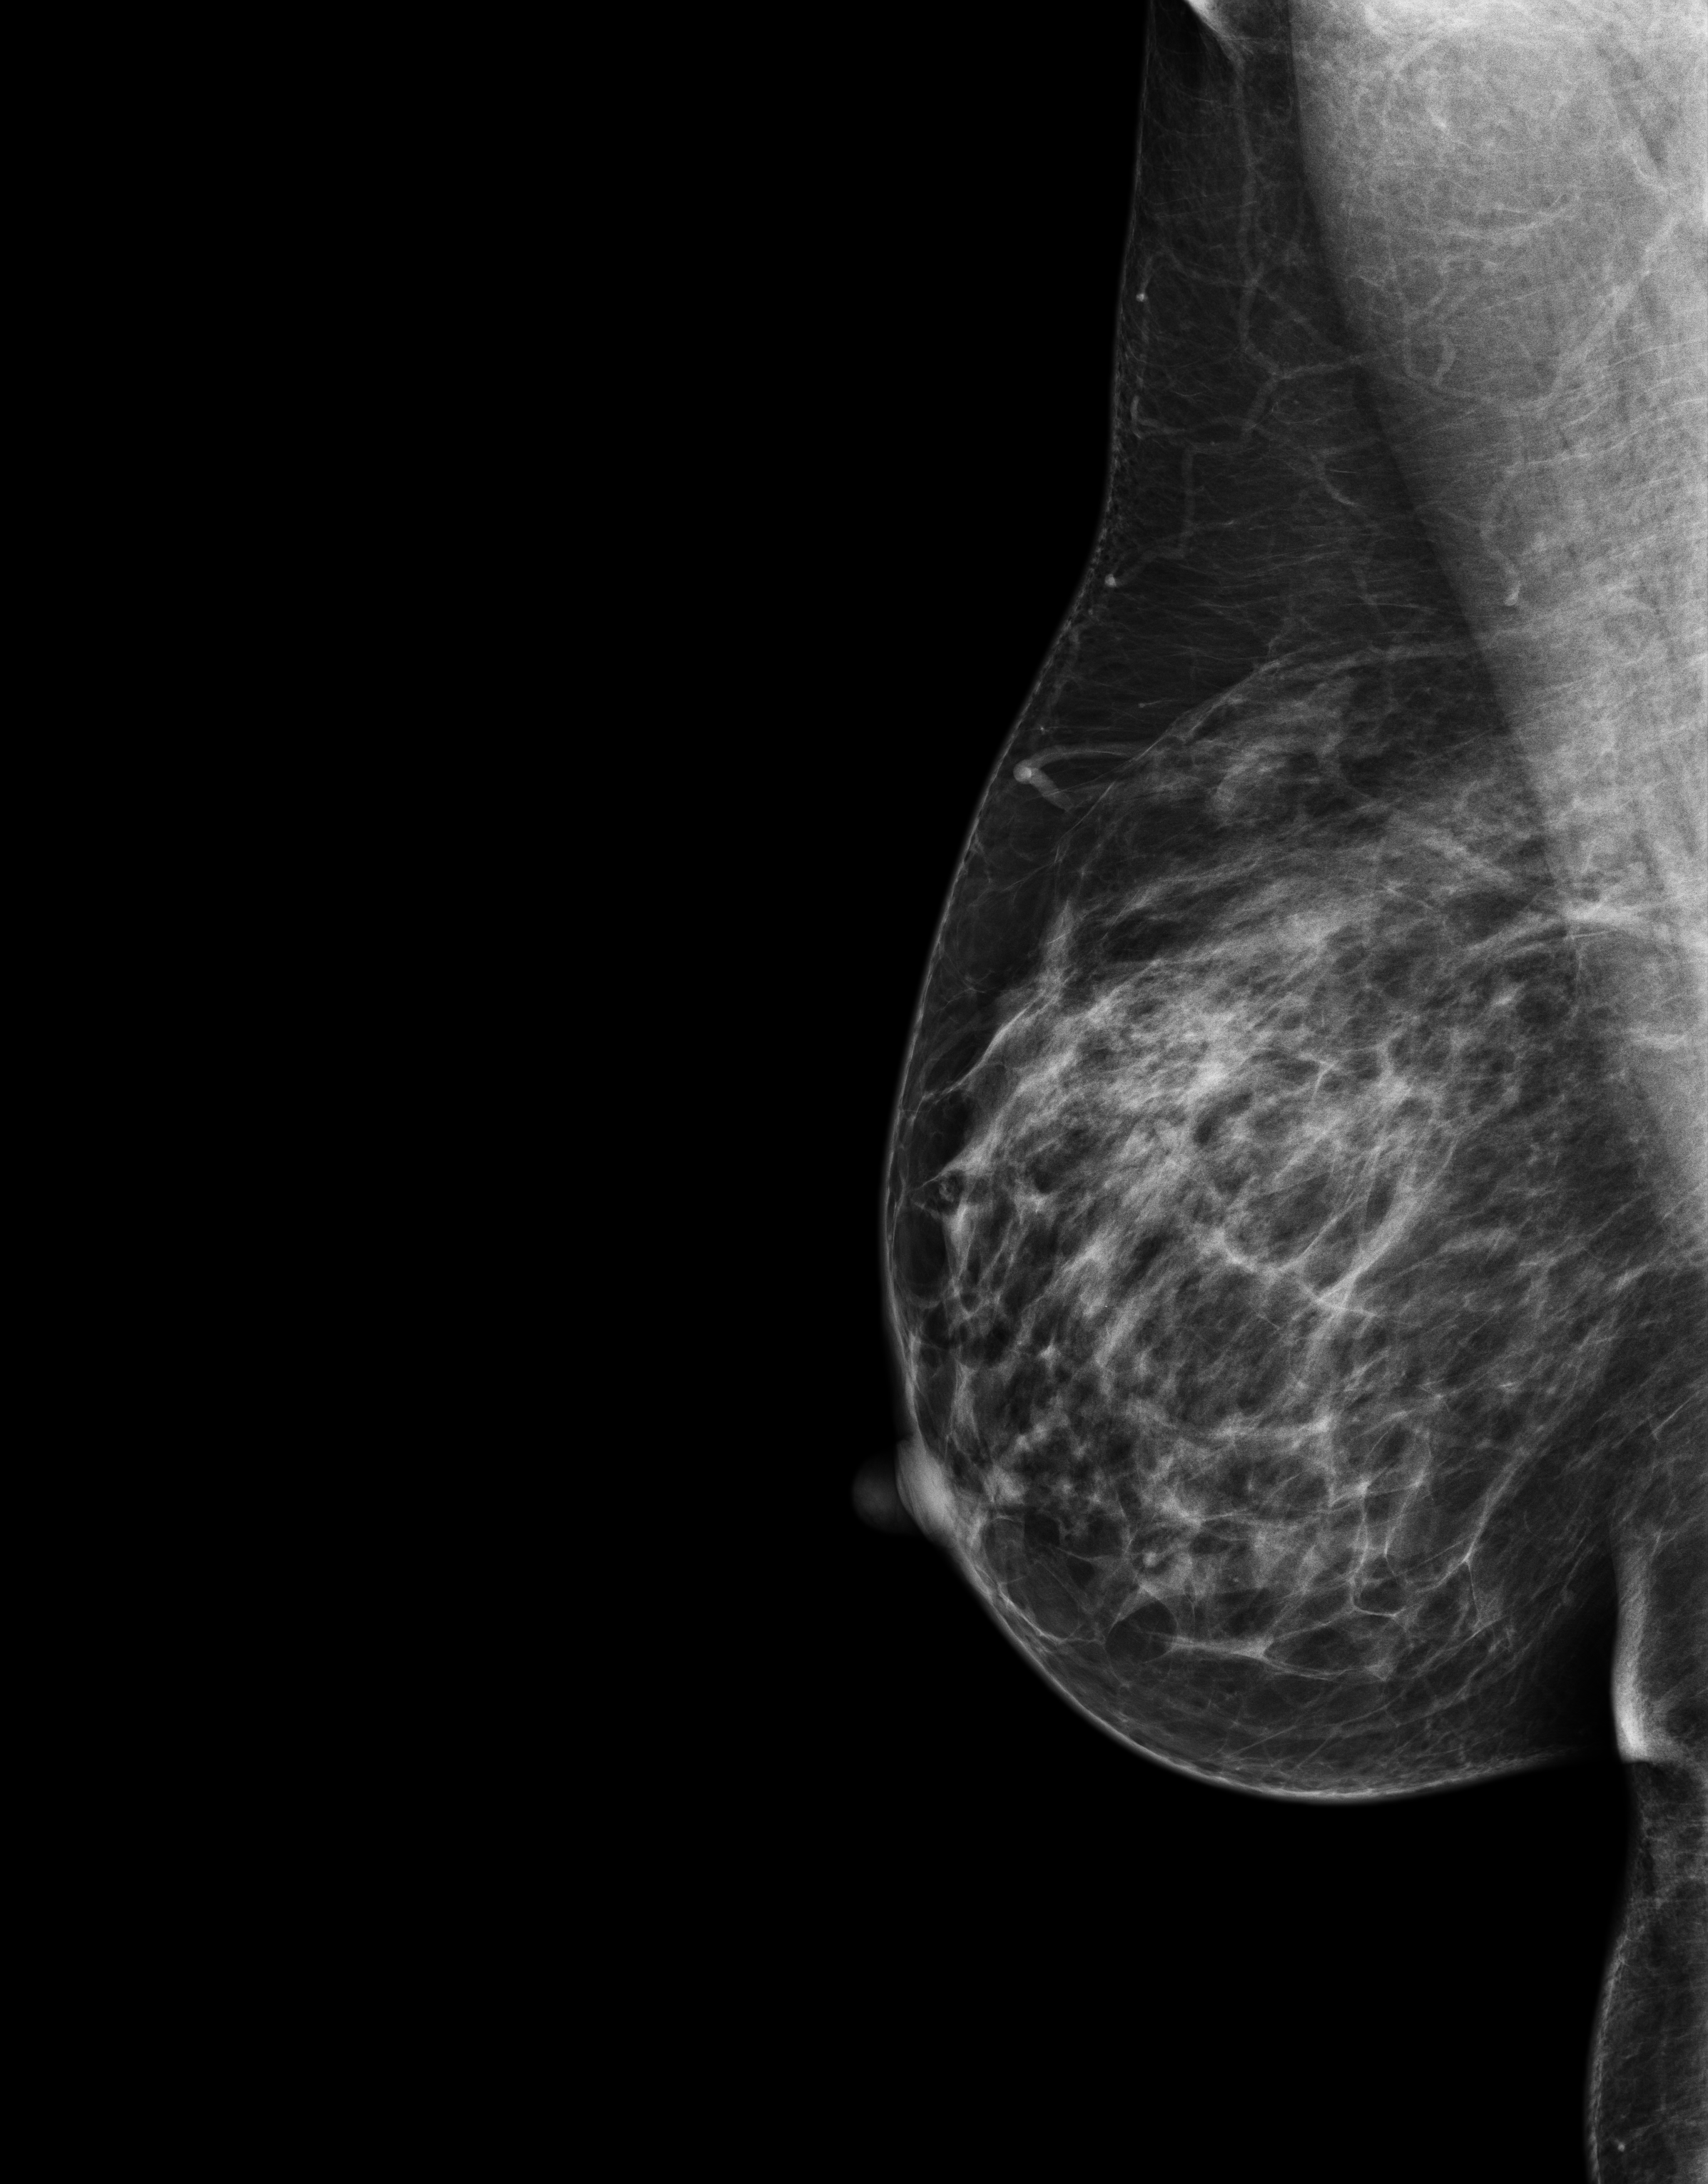
Screening examination. Patient: female, 50 years.
Image type: full-field digital mammogram. Breast: right. Projection: mediolateral oblique (MLO) view.